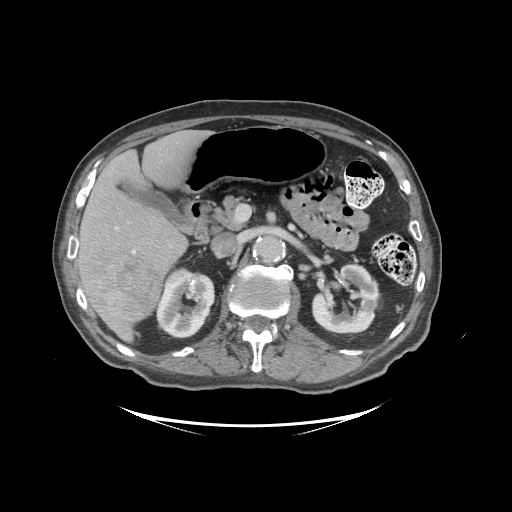
Contrast-enhanced abdominal CT (liver protocol), one axial slice. Position 52 of 99 along the scan axis. Reconstruction kernel STANDARD. 140 kVp. Soft-tissue window (W 400 / L 40 HU). 2.5 mm slice thickness. 512 × 512 image matrix. Case-level facts recorded for this patient, not image findings: diagnosis: hepatocellular carcinoma (patient treated with transarterial chemoembolisation; whether this scan precedes or follows treatment is not stated here); TNM stage (as recorded): Stage-I; Child-Pugh class: A; tumour differentiation: moderately differentiated.
Annotated regions visible in this slice (semi-automatically segmented with operator editing):
- liver parenchyma outside the tumour (the mass and vessels are separate outlines, so this box may not span the whole liver): bounding box (x1, y1, x2, y2) in pixels: (72, 130, 210, 340)
- mass: (89, 257, 164, 323)
- liver vessels: (74, 227, 136, 256)